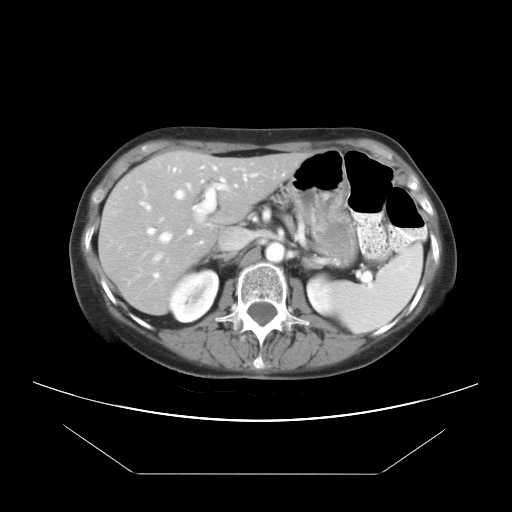
Contrast-enhanced abdominal CT, one axial slice. Position 13 of 21 along the scan axis. Reconstruction kernel STANDARD. 120 kVp. Soft-tissue window (W 400 / L 40 HU). 7.5 mm slice thickness. 512 × 512 image matrix. Female patient, age 72 years. From the clinical record (not read from this slice): diagnosis: colorectal cancer liver metastases, imaged before liver resection; multiple liver metastases: yes; largest metastasis: 4 cm; disease in both lobes: yes.
Annotated regions visible in this slice (expert manual segmentation):
- hepatic veins: box from (x=153, y=167) to (x=247, y=262) px
- liver: (x=100, y=152)–(x=303, y=313)
- planned liver remnant (the part of the liver to remain after resection): (x=100, y=152)–(x=303, y=281)
- portal vein (with intrahepatic branches): (x=140, y=184)–(x=237, y=277)